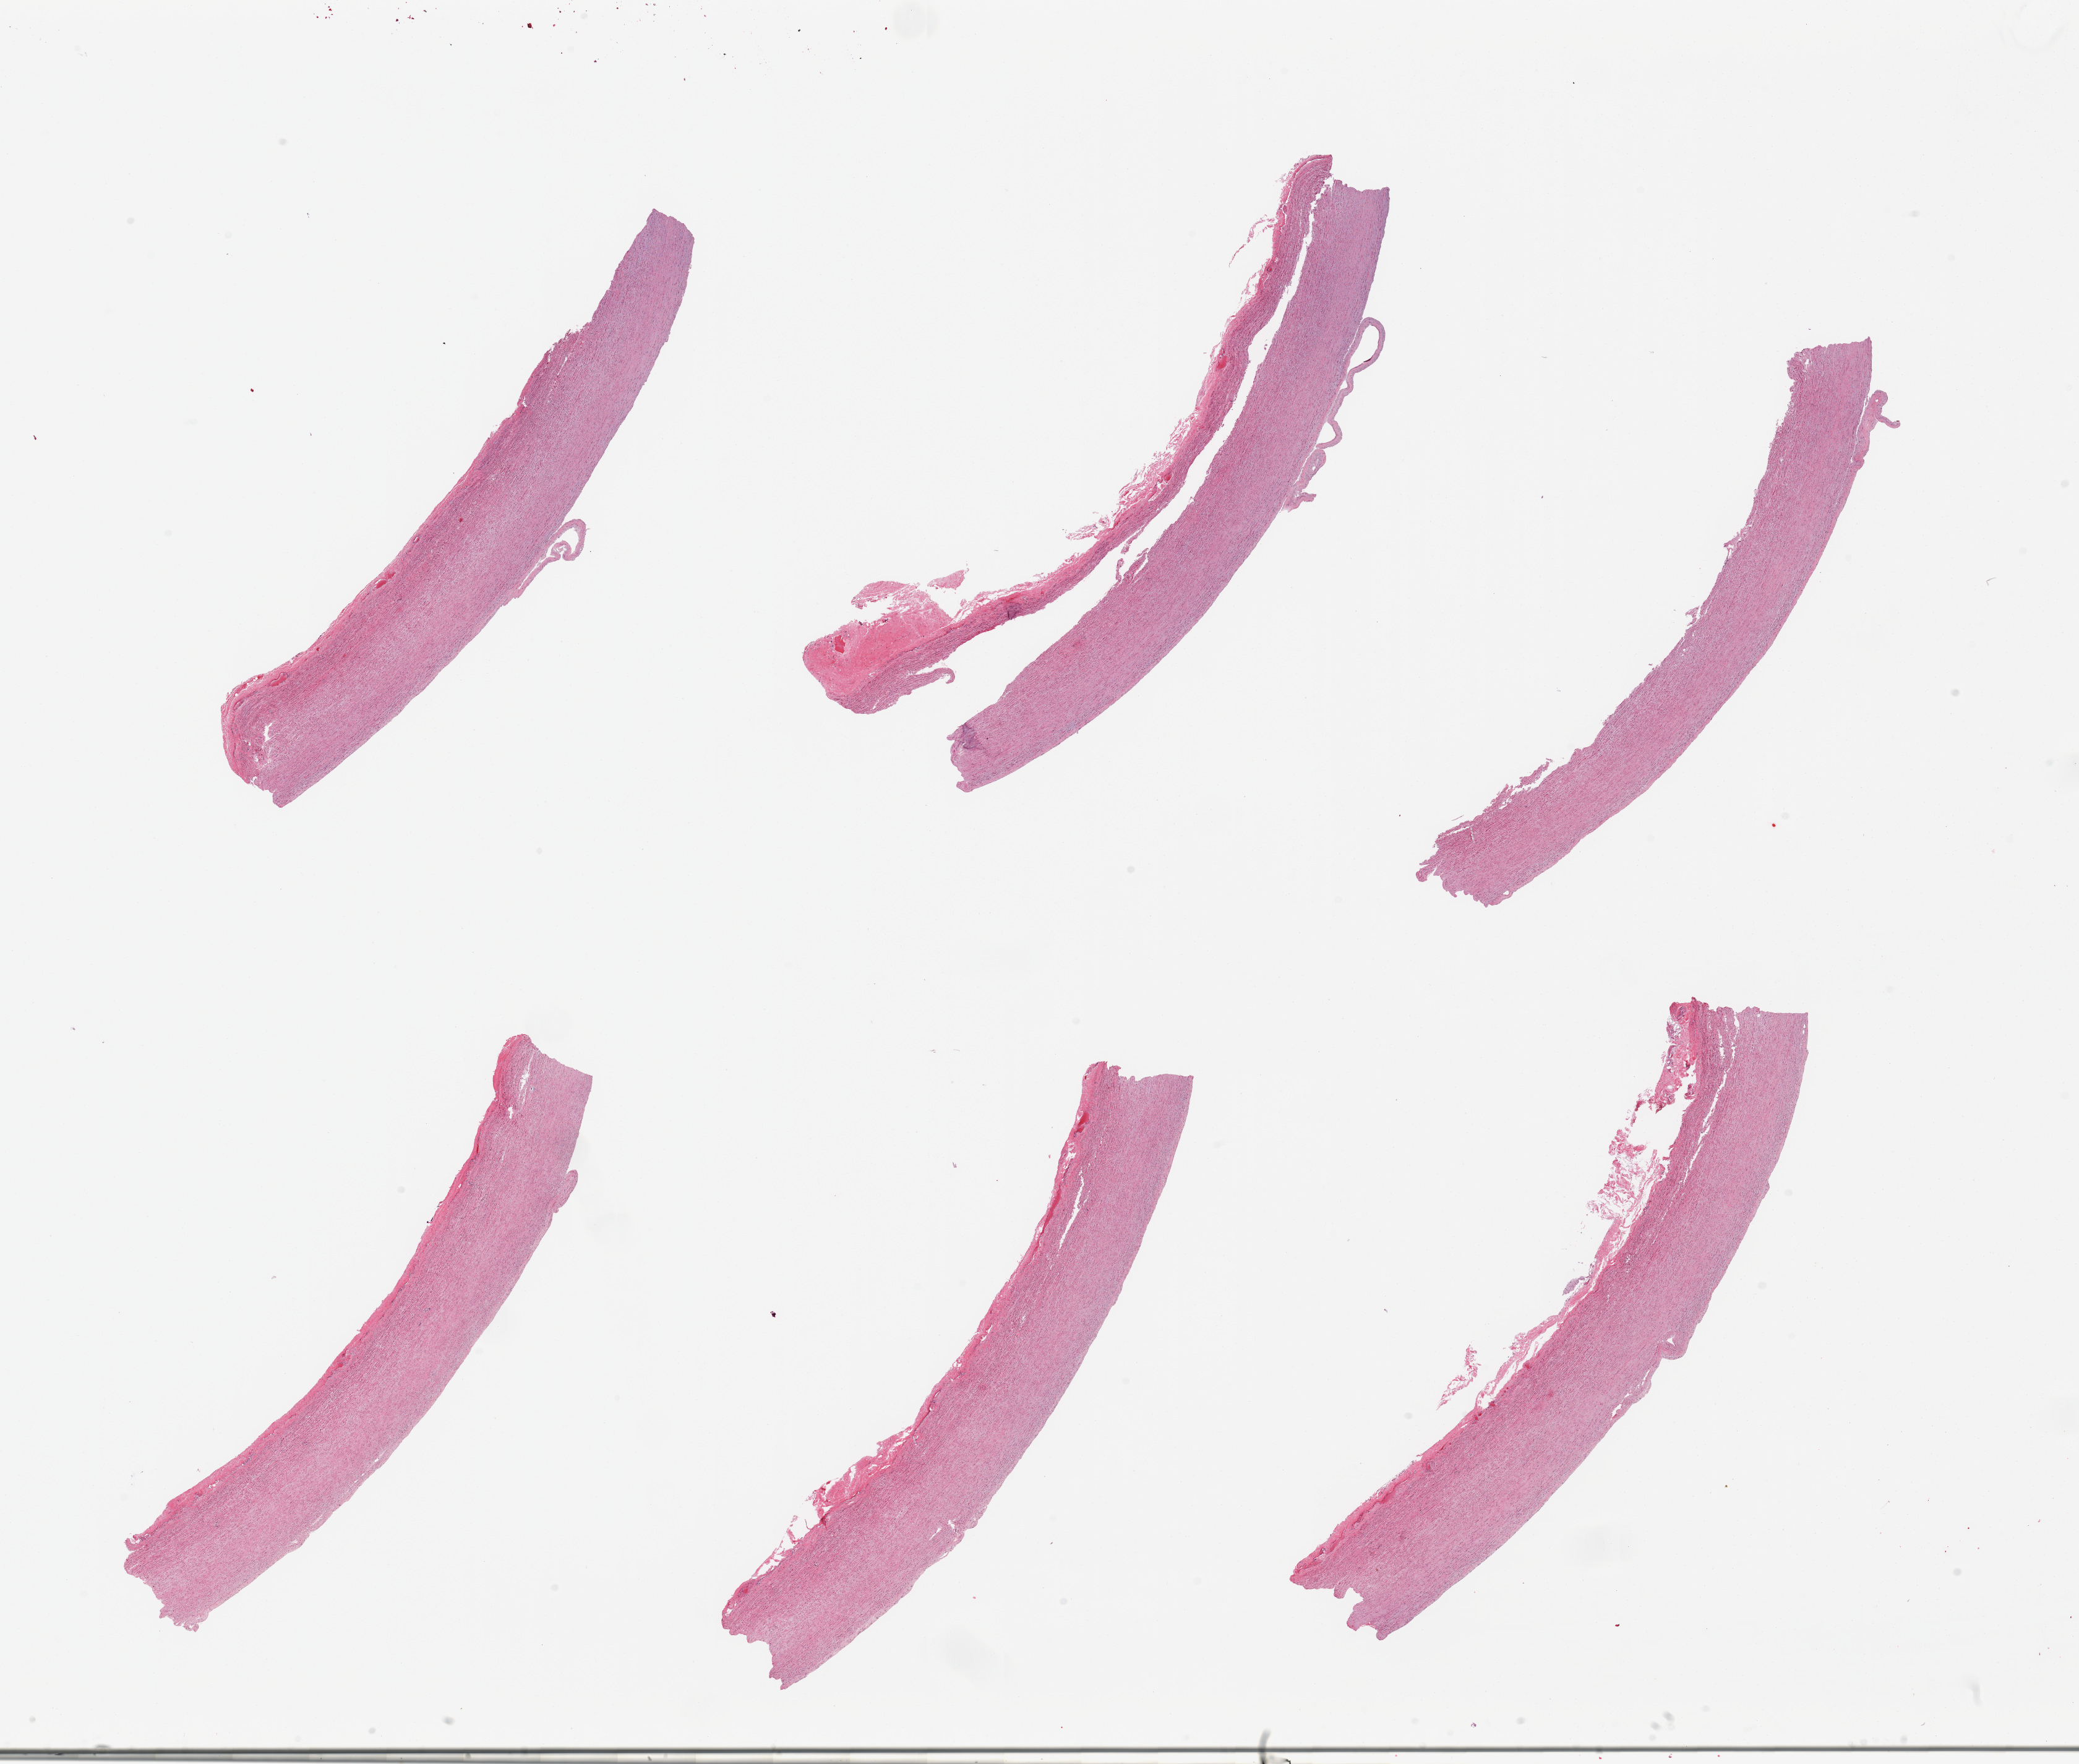
Haematoxylin and eosin whole-slide image, brightfield, a low-resolution overview of the entire scanned area, about 26.6 x 22.6 mm (acquisition: 20x scan). PAXgene-fixed, paraffin-embedded tissue. Section of aorta (target tissue). Tissue donor sample. Male donor.
Reviewer comment on this tissue sample: 6 pieces, minimal atherosis.